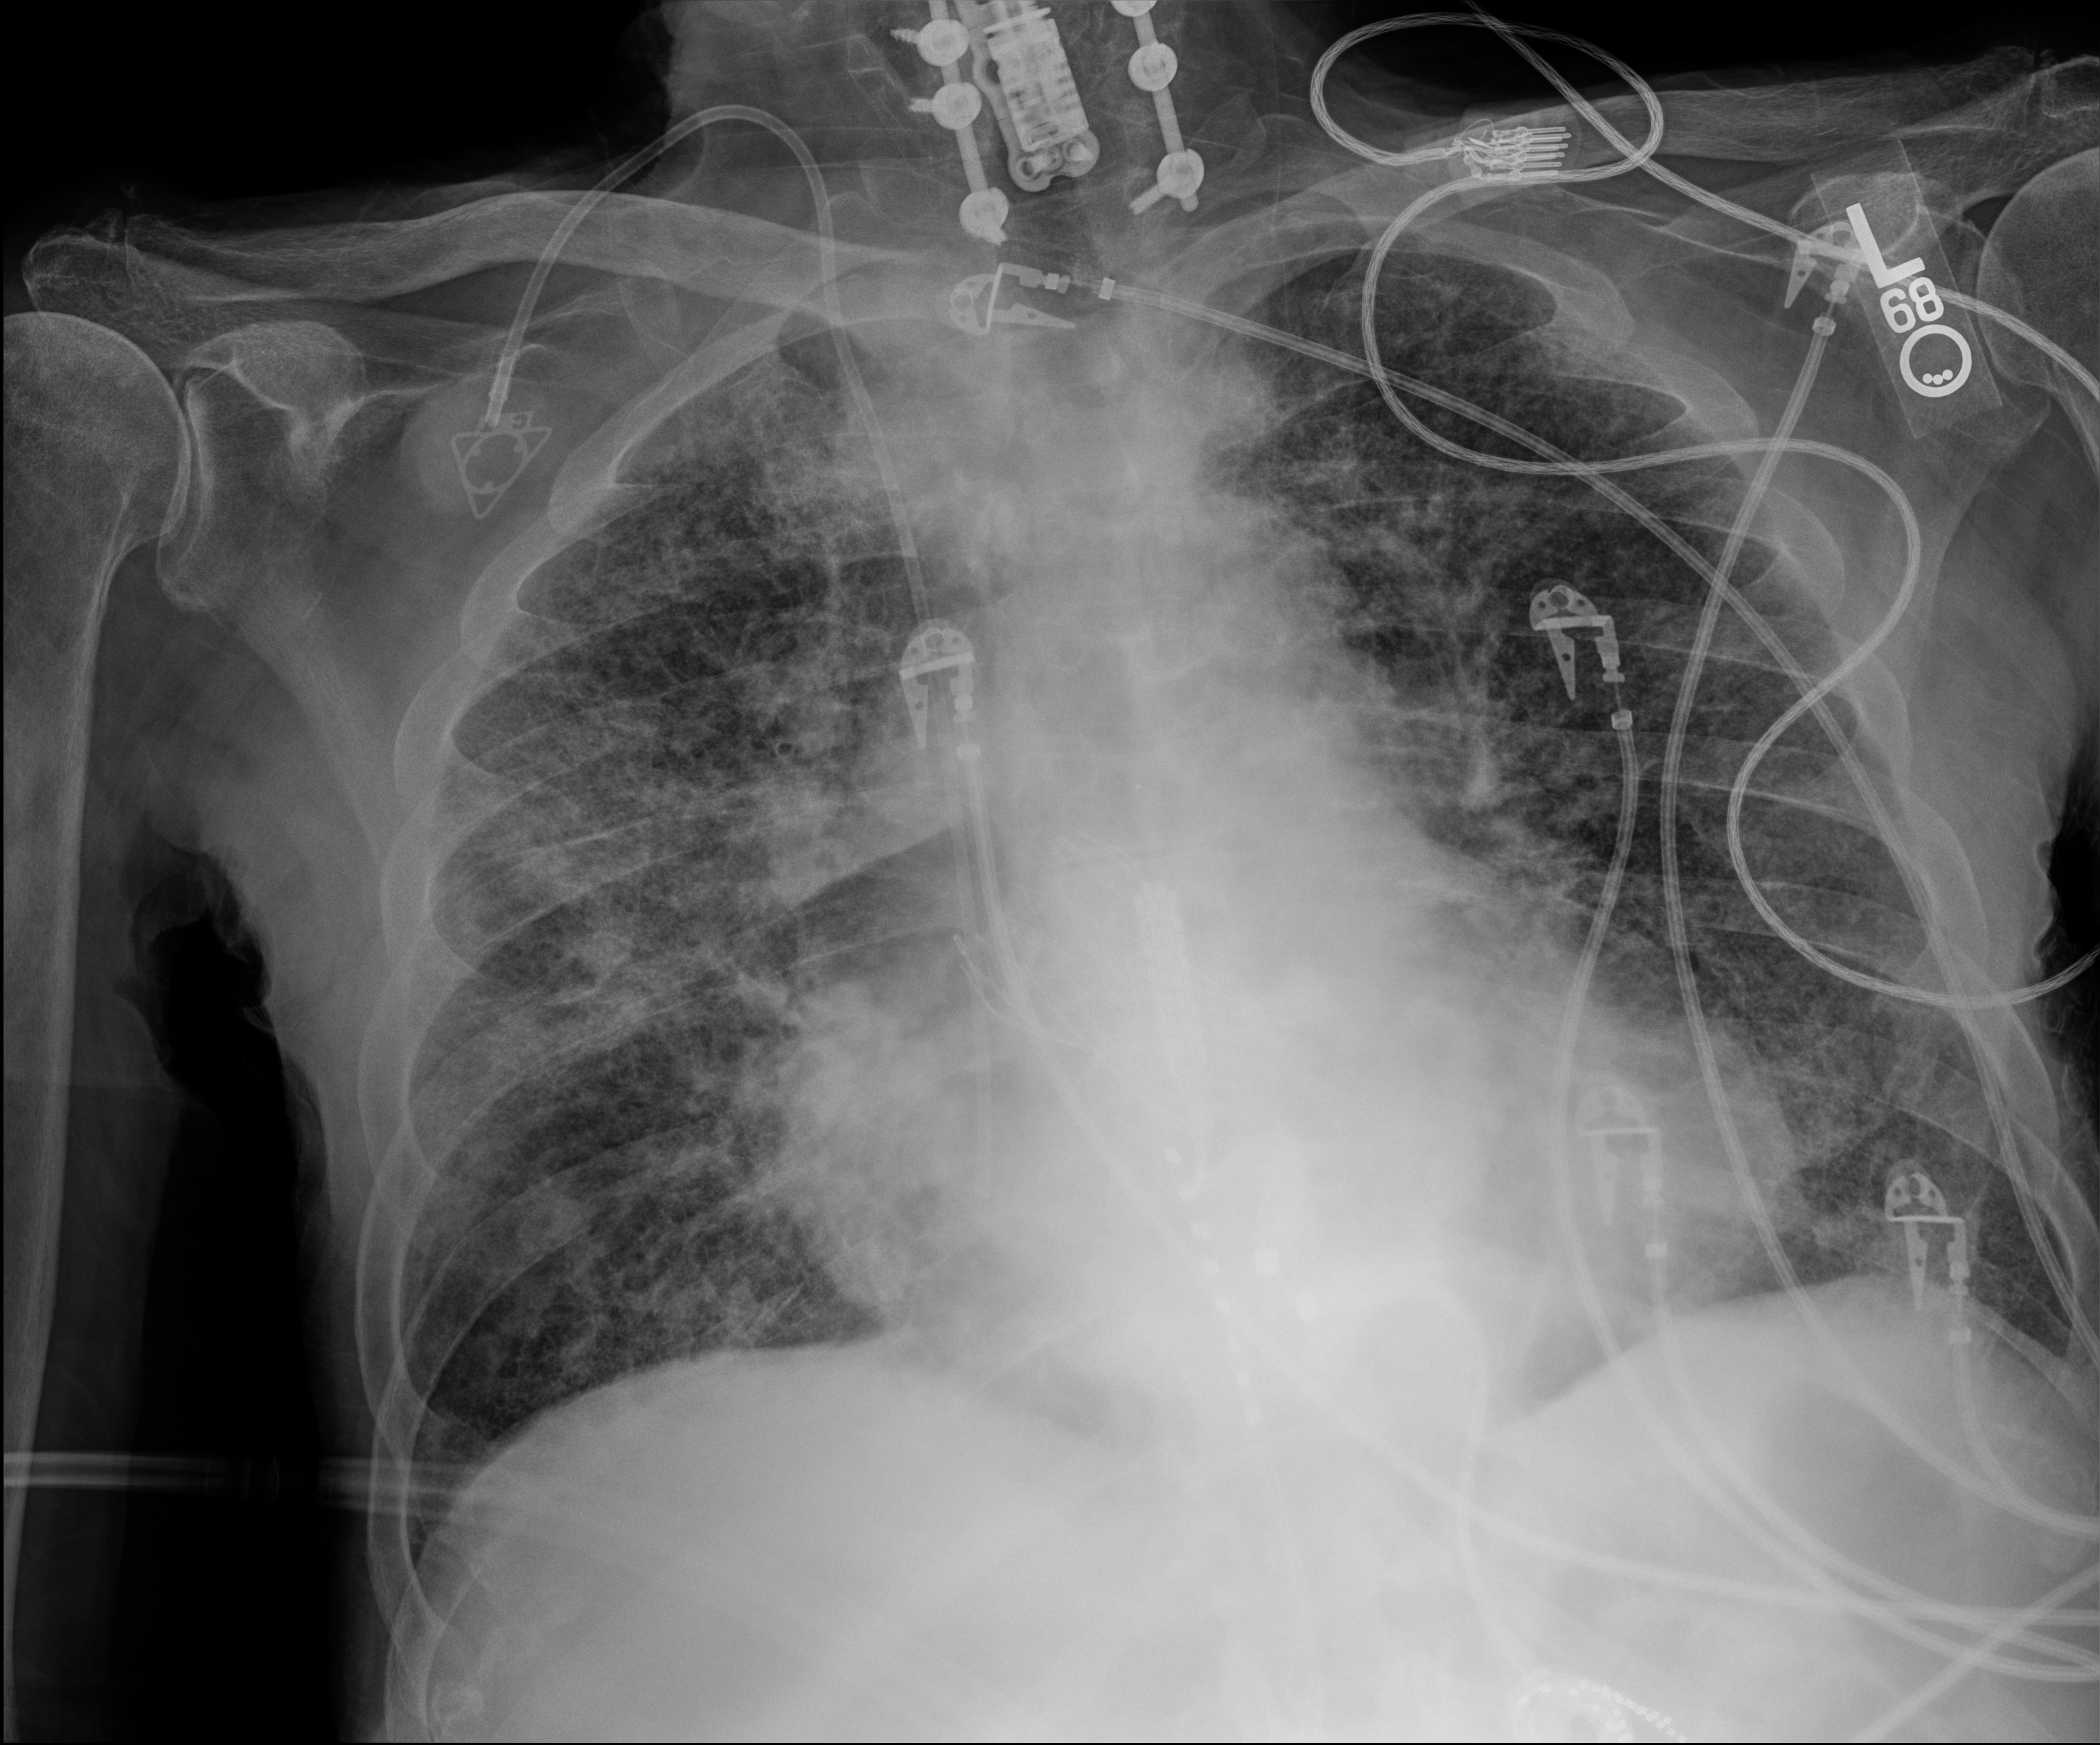
Chest radiograph; anteroposterior (AP) projection. Male patient hospitalised with COVID-19, age 75–90 years.
Hospital-stay facts (about this admission, not read from this image; timing relative to this image not recorded): mechanically ventilated during this hospital stay: no; admitted to intensive care during this hospital stay: yes.